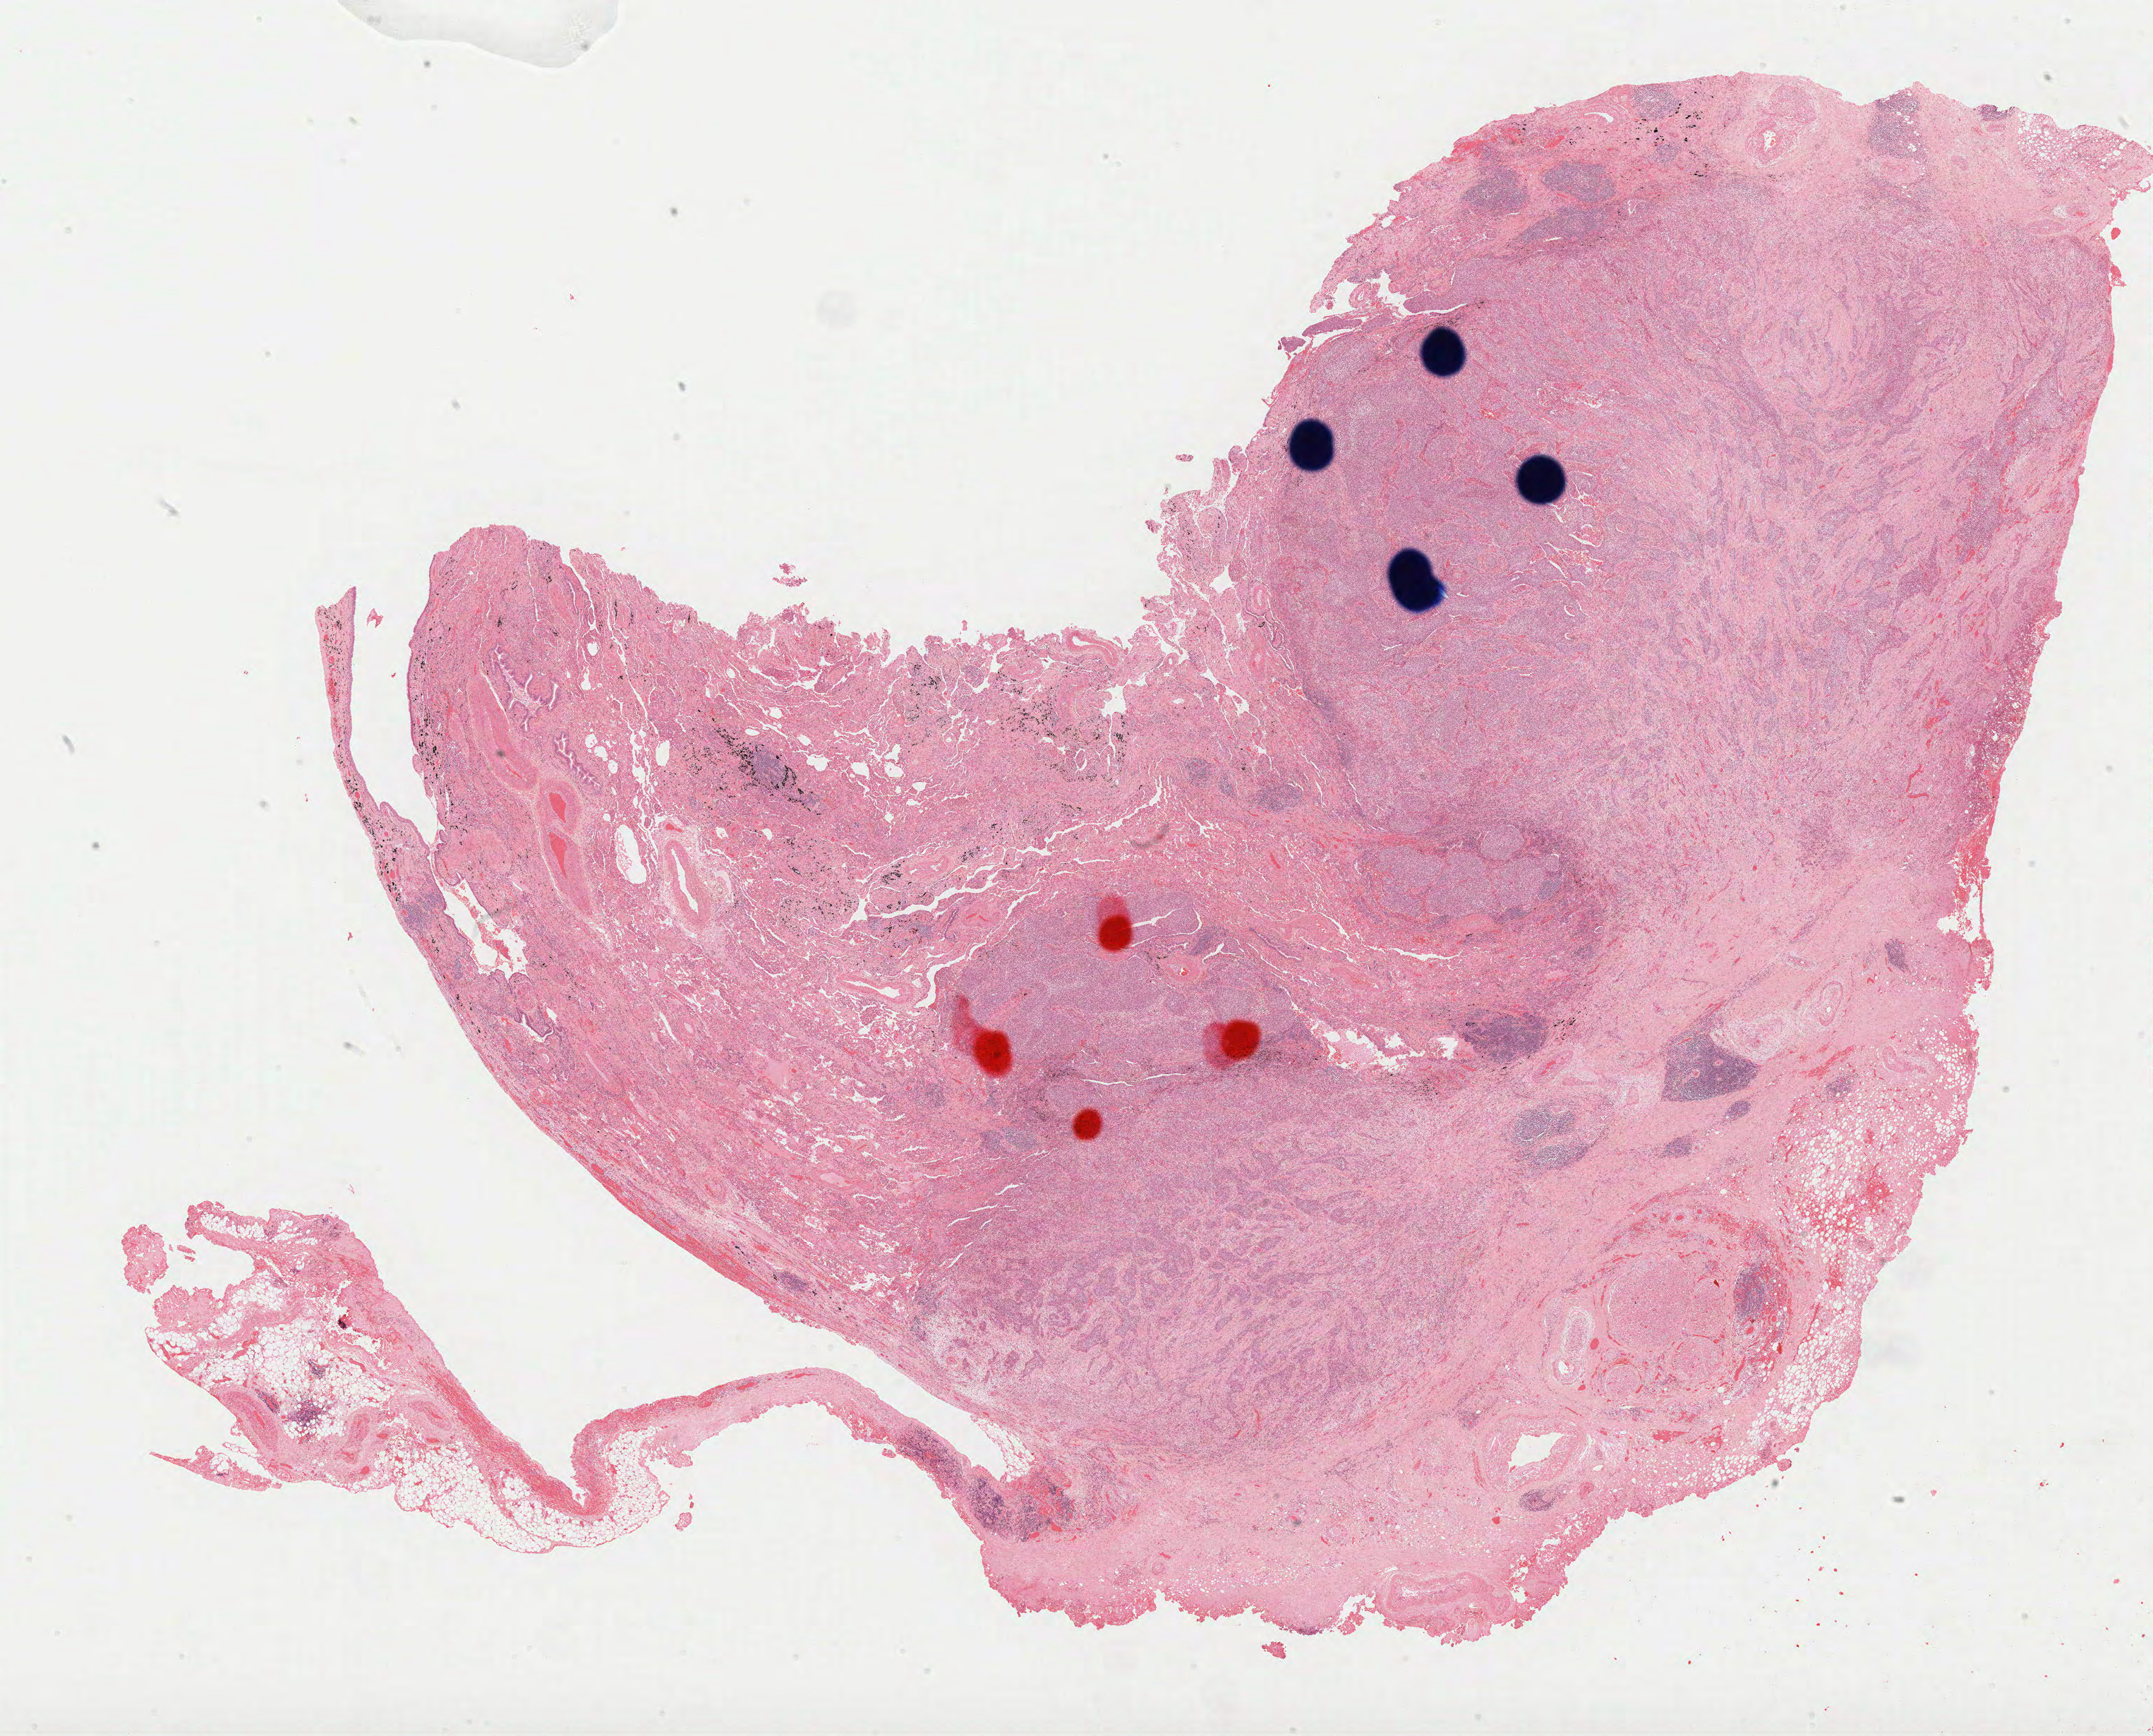
H&E-stained whole-slide image, a low-resolution overview of the entire scanned area, about 24.6 x 19.8 mm (acquisition: 40x scan); formalin-fixed paraffin-embedded (FFPE) diagnostic section; lung, primary tumour sample. Male patient; age at initial diagnosis 73 years.
Laterality: right. Diagnosis: Squamous cell carcinoma, NOS. AJCC pathologic stage: IV.